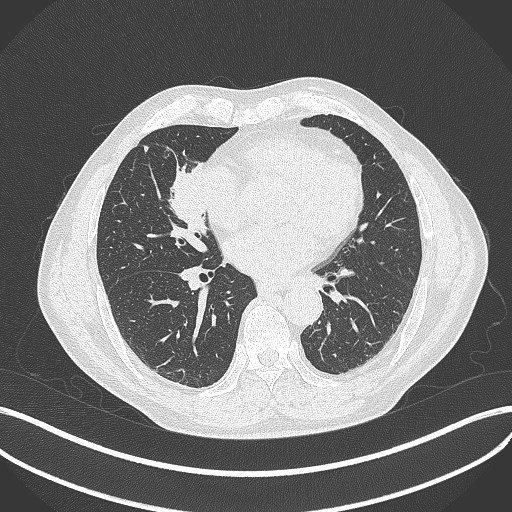
Chest CT, one axial slice; position 178 of 429 along the scan axis; reconstruction kernel B70f; 120 kVp; lung window (W 1500 / L -600 HU); 1 mm slice thickness; 512 × 512 image matrix. Male patient, age 61 years. Case-level facts recorded for this patient, not image findings: clinical TNM (as recorded): T2b N1 M0.
Outlined on this slice (bounding box drawn by a radiologist):
- lung tumour (recorded histology: squamous cell carcinoma): bounding box (x1, y1, x2, y2) in pixels: (165, 153, 216, 242)